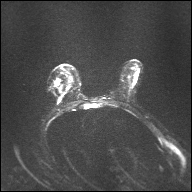
Breast MRI, one axial slice; slice 21 of 32 in the series (ordered by position); diffusion-weighted series; image 2 of 4 stored at this slice position (different b-values; order by instance number); 1.5 T; 4 mm slice thickness; 192 × 192 image matrix, field of view 360 × 360 mm. Female patient.
Outlined on this slice (expert manual segmentation):
- tumour on diffusion-weighted imaging: box from (x=55, y=81) to (x=59, y=86) px